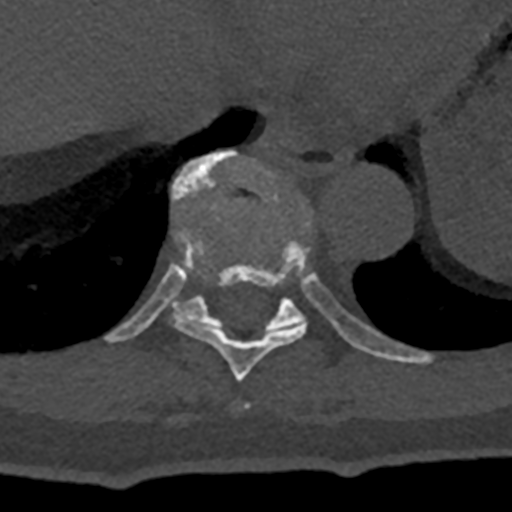
CT including the spine, one axial slice. Position 635 of 797 along the scan axis. Reconstruction kernel Br40s/3. 120 kVp. Bone window (W 1800 / L 400 HU). 0.5 mm slice thickness. 512 × 512 image matrix. Patient: male, 74 years. Case-level facts recorded for this patient, not image findings: primary cancer: renal.
Outlined on this slice (semi-automatically segmented with operator editing):
- T10 vertebra: bounding box <106,150,430,363> (left, top, right, bottom; pixels)
- T9 vertebra: <170,227,307,381>